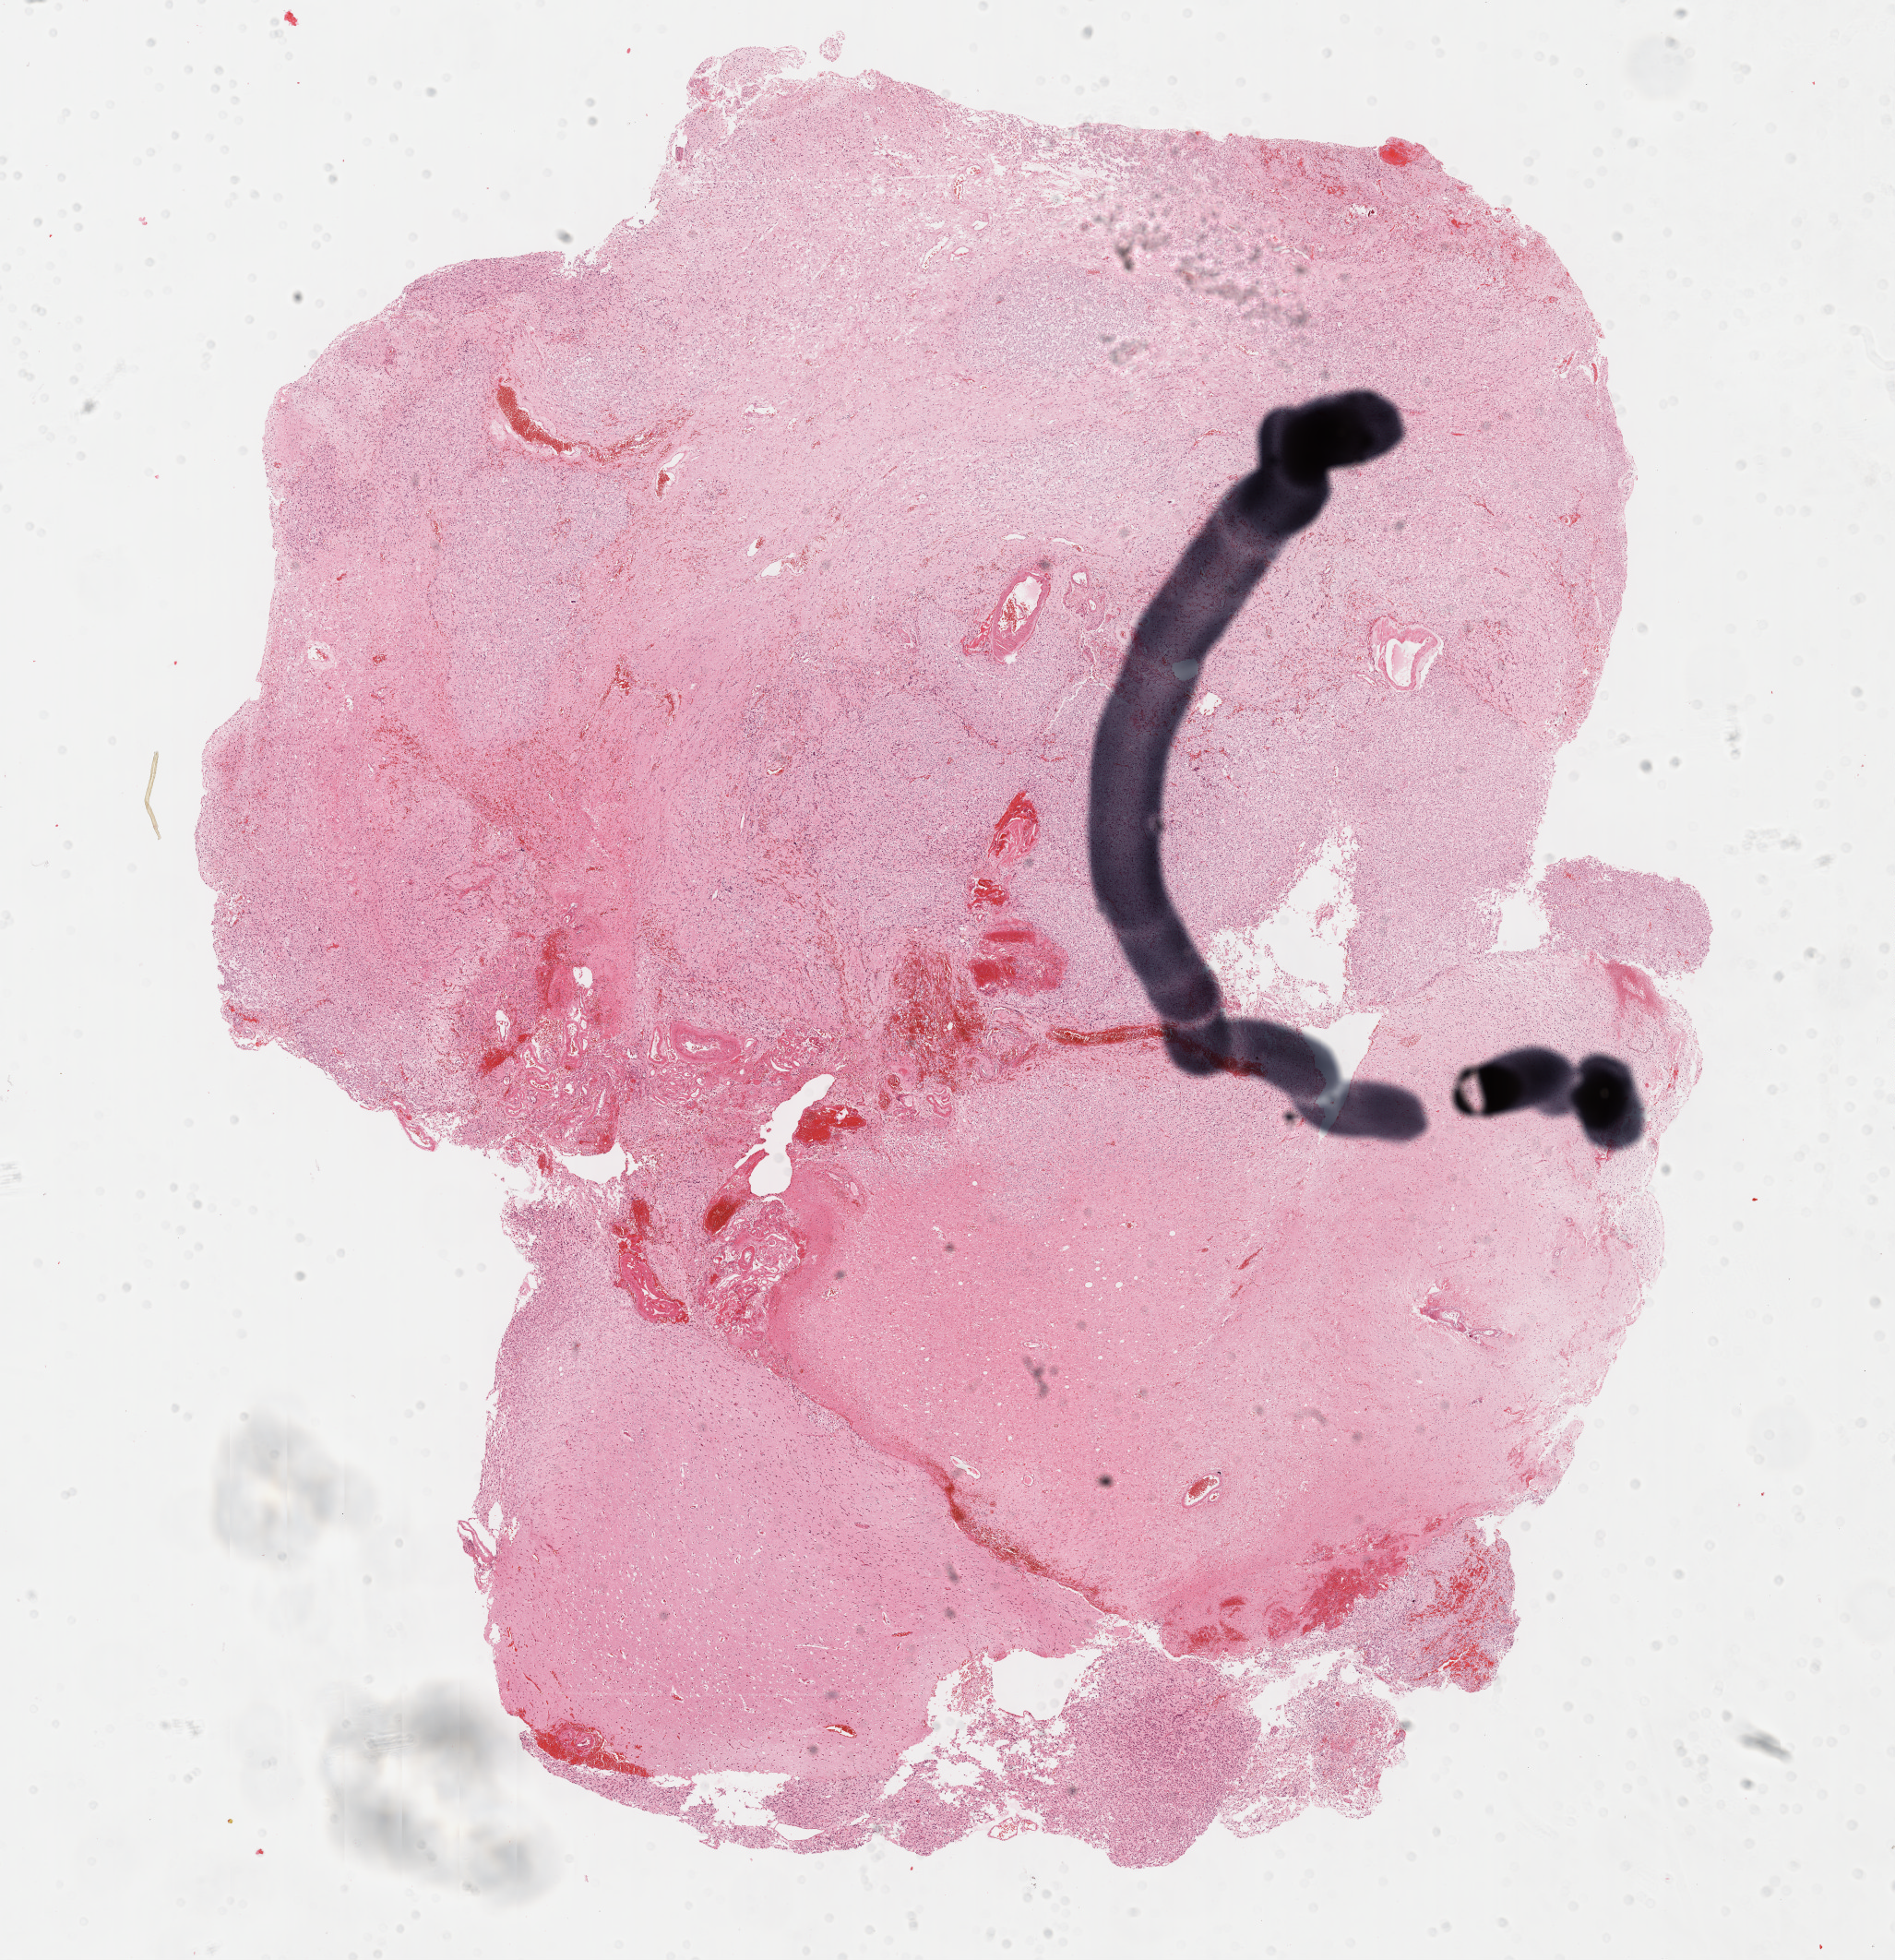
Whole-slide histology image, H&E — shown as a low-resolution overview of the whole scanned area (about 16.6 x 17.2 mm). FFPE section. Primary tumour sample from the brain. Female, age 73 years at initial diagnosis.
Pathologic diagnosis: Mixed glioma (cerebrum).